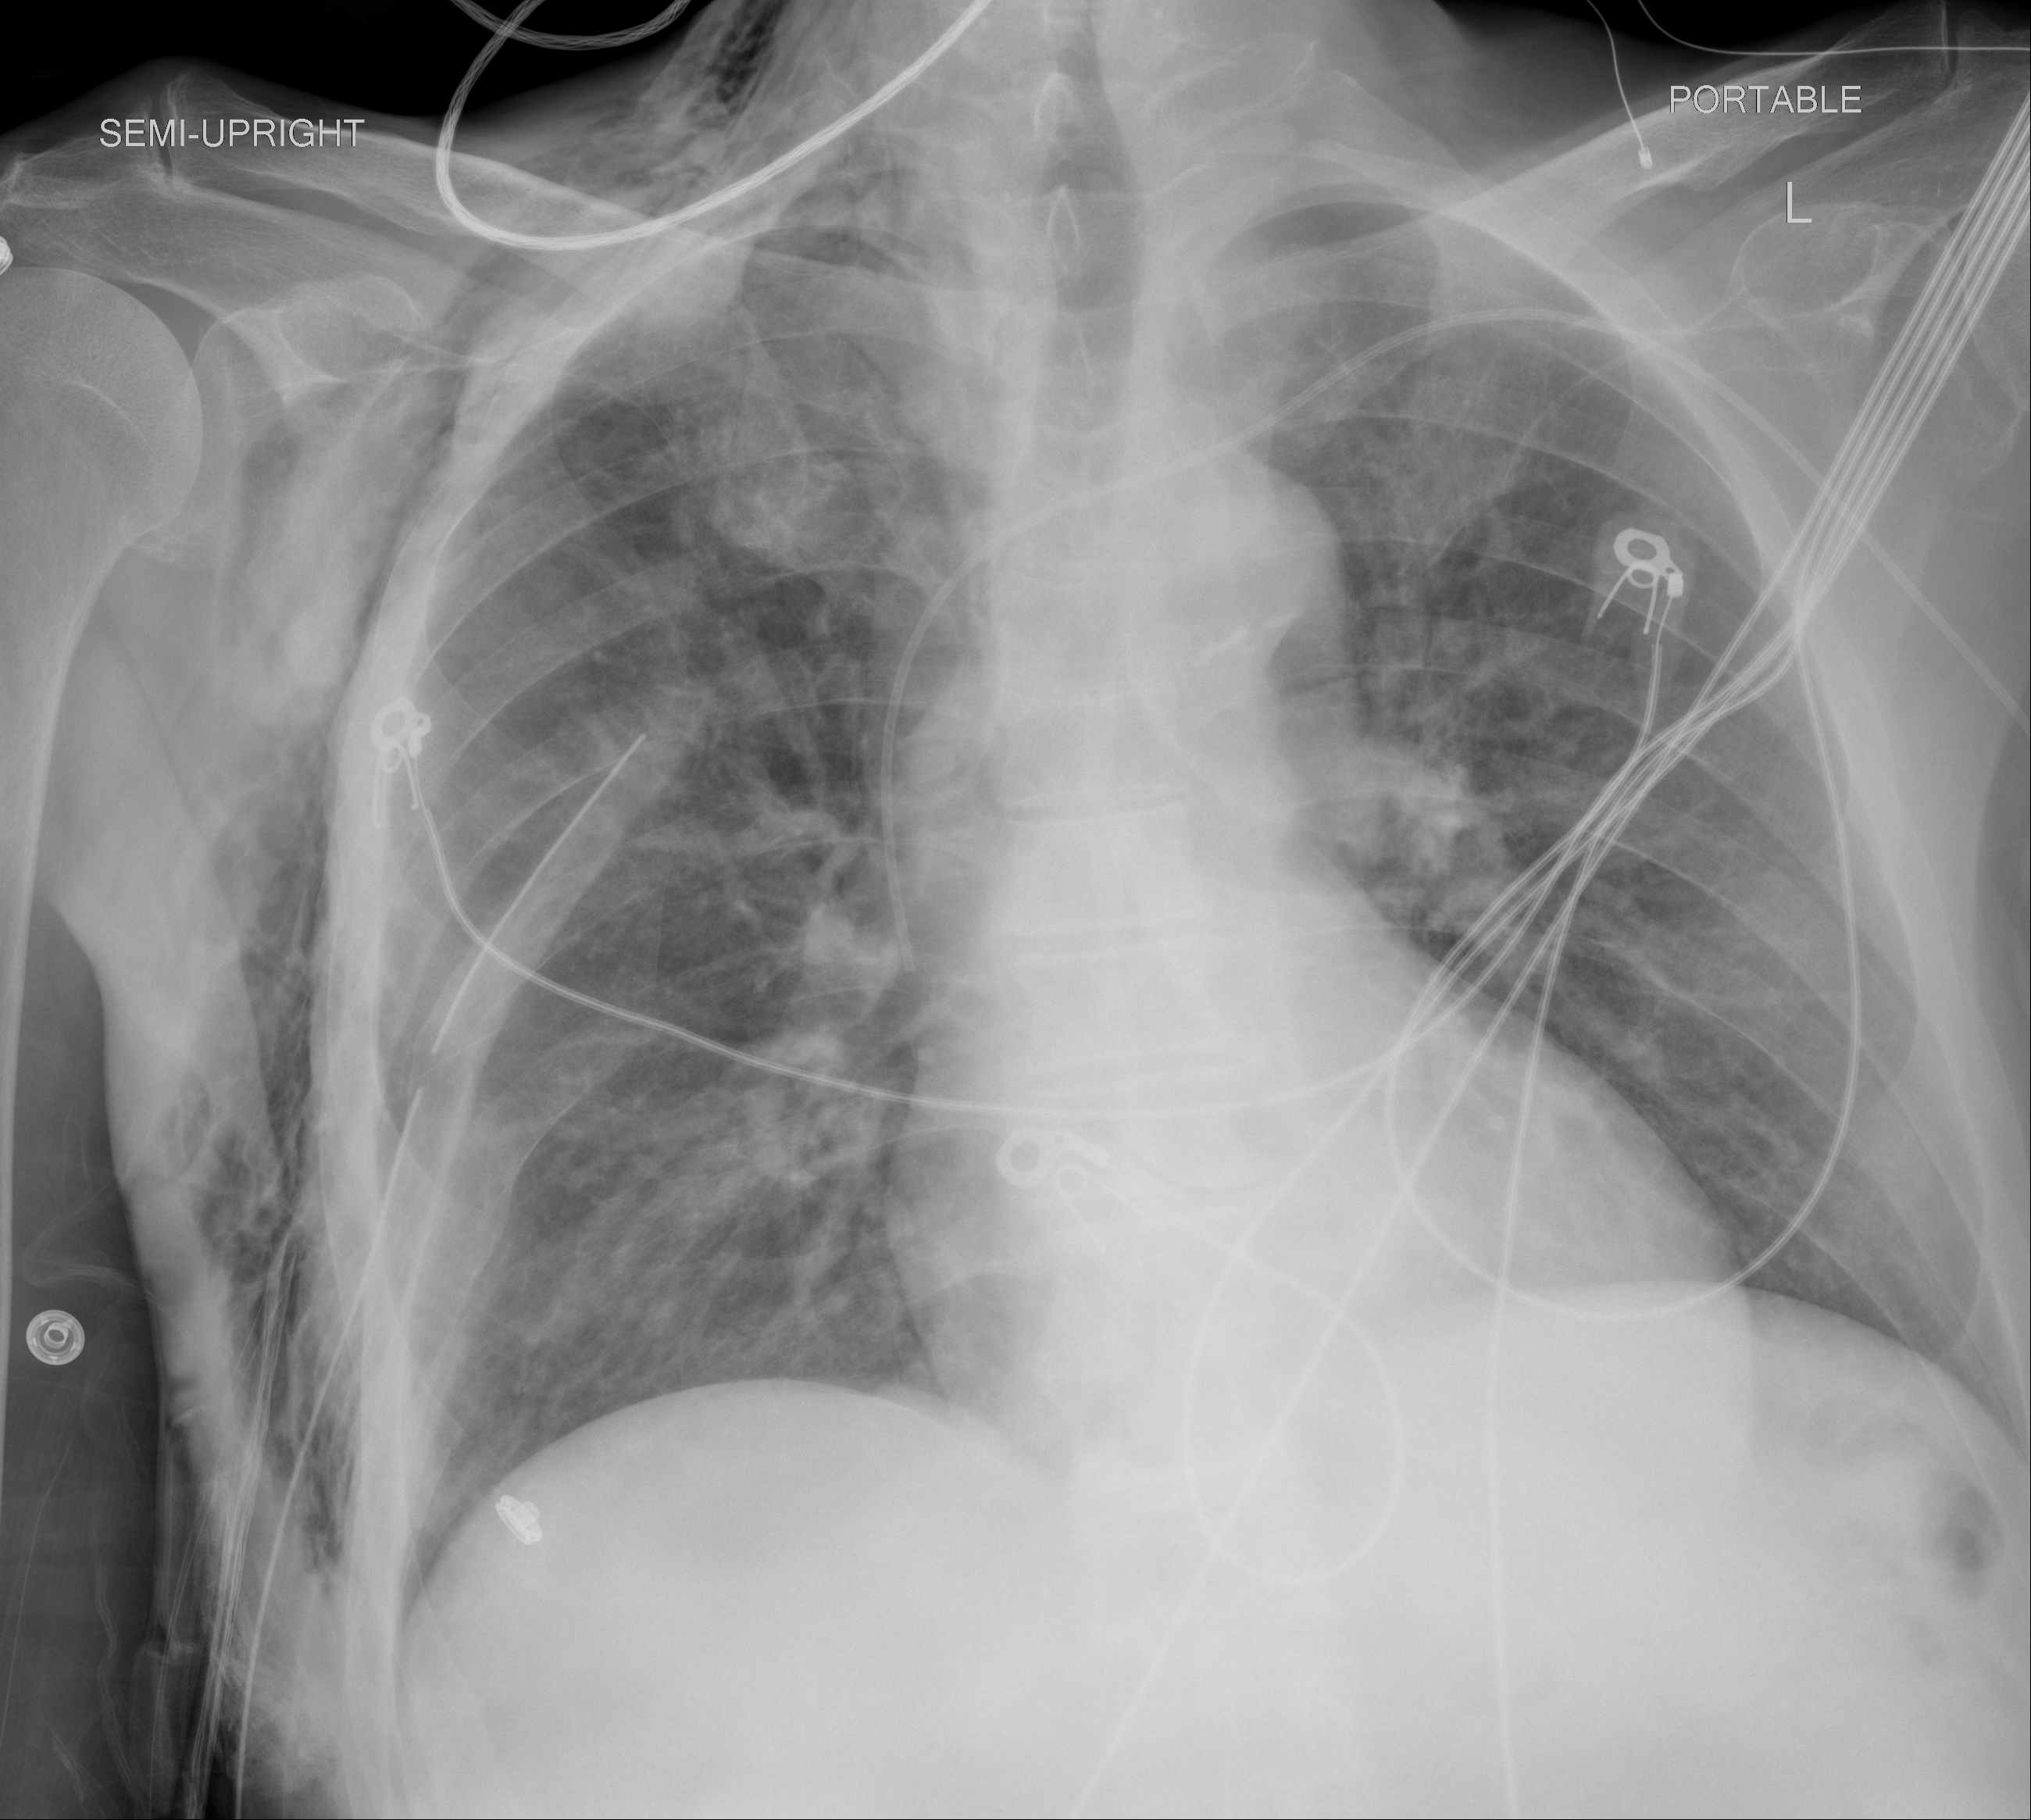
Portable chest radiograph, AP projection. Male patient, age 59 years; imaged 4 days after the COVID-19 diagnosis.
Key findings recorded by the radiologist: Mild atelectatic changes at the right lung base. There is no focal consolidation. The left lung appears clear.